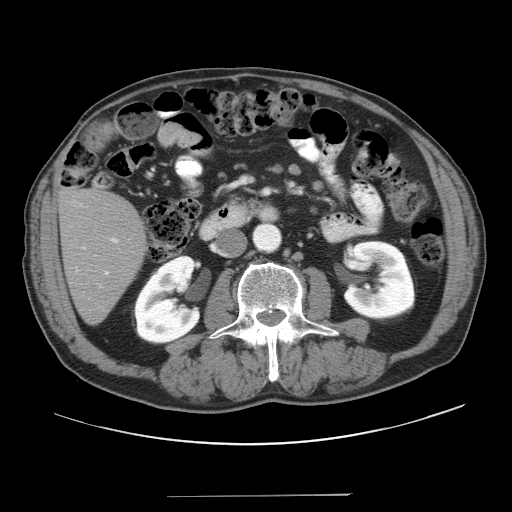
Contrast-enhanced abdominal CT, one axial slice; position 8 of 41 along the scan axis; reconstruction kernel STANDARD; intravenous contrast given; soft-tissue window (W 400 / L 40 HU); 512 × 512 image matrix. Male patient, age 75 years. Case-level facts recorded for this patient, not image findings: diagnosis: colorectal cancer liver metastases, imaged before liver resection; multiple liver metastases: no; largest metastasis: 5.2 cm; chemotherapy before resection: no.
Outlined on this slice (manually delineated by an expert):
- liver: bounding box (x1, y1, x2, y2) in pixels: (60, 189, 146, 321)
- planned liver remnant (the part of the liver to remain after resection): (60, 189, 146, 321)
- portal vein (with intrahepatic branches): (104, 237, 119, 276)